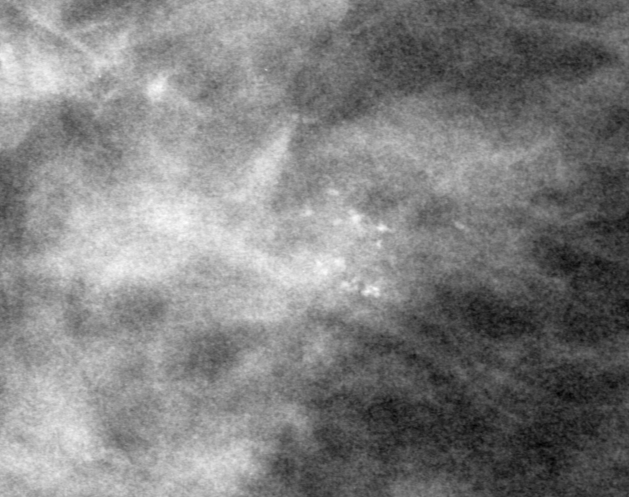
Cropped region of a digitized screen-film mammogram centred on a radiologist-marked abnormality; right breast; CC view; BI-RADS breast density category 2 (scale 1–4).
Calcifications, morphology pleomorphic, distribution clustered; BI-RADS assessment category 0; subtlety rating 5 on a 1 (subtle) to 5 (obvious) scale; pathology (as recorded): benign.